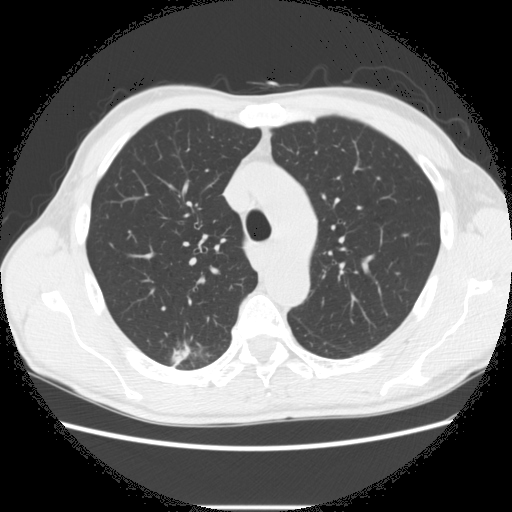
Low-dose screening chest CT, one axial slice. Slice 205 of 282 in the series (ordered by position). Reconstruction kernel STANDARD. Lung window (W 1500 / L -600 HU). 2.5 mm slice thickness. 512 × 512 image matrix.
Annotated regions visible in this slice (manually delineated by an expert):
- lesion 1 (tumor, upper lobe of right lung): bounding box (x1, y1, x2, y2) in pixels: (171, 343, 190, 367)